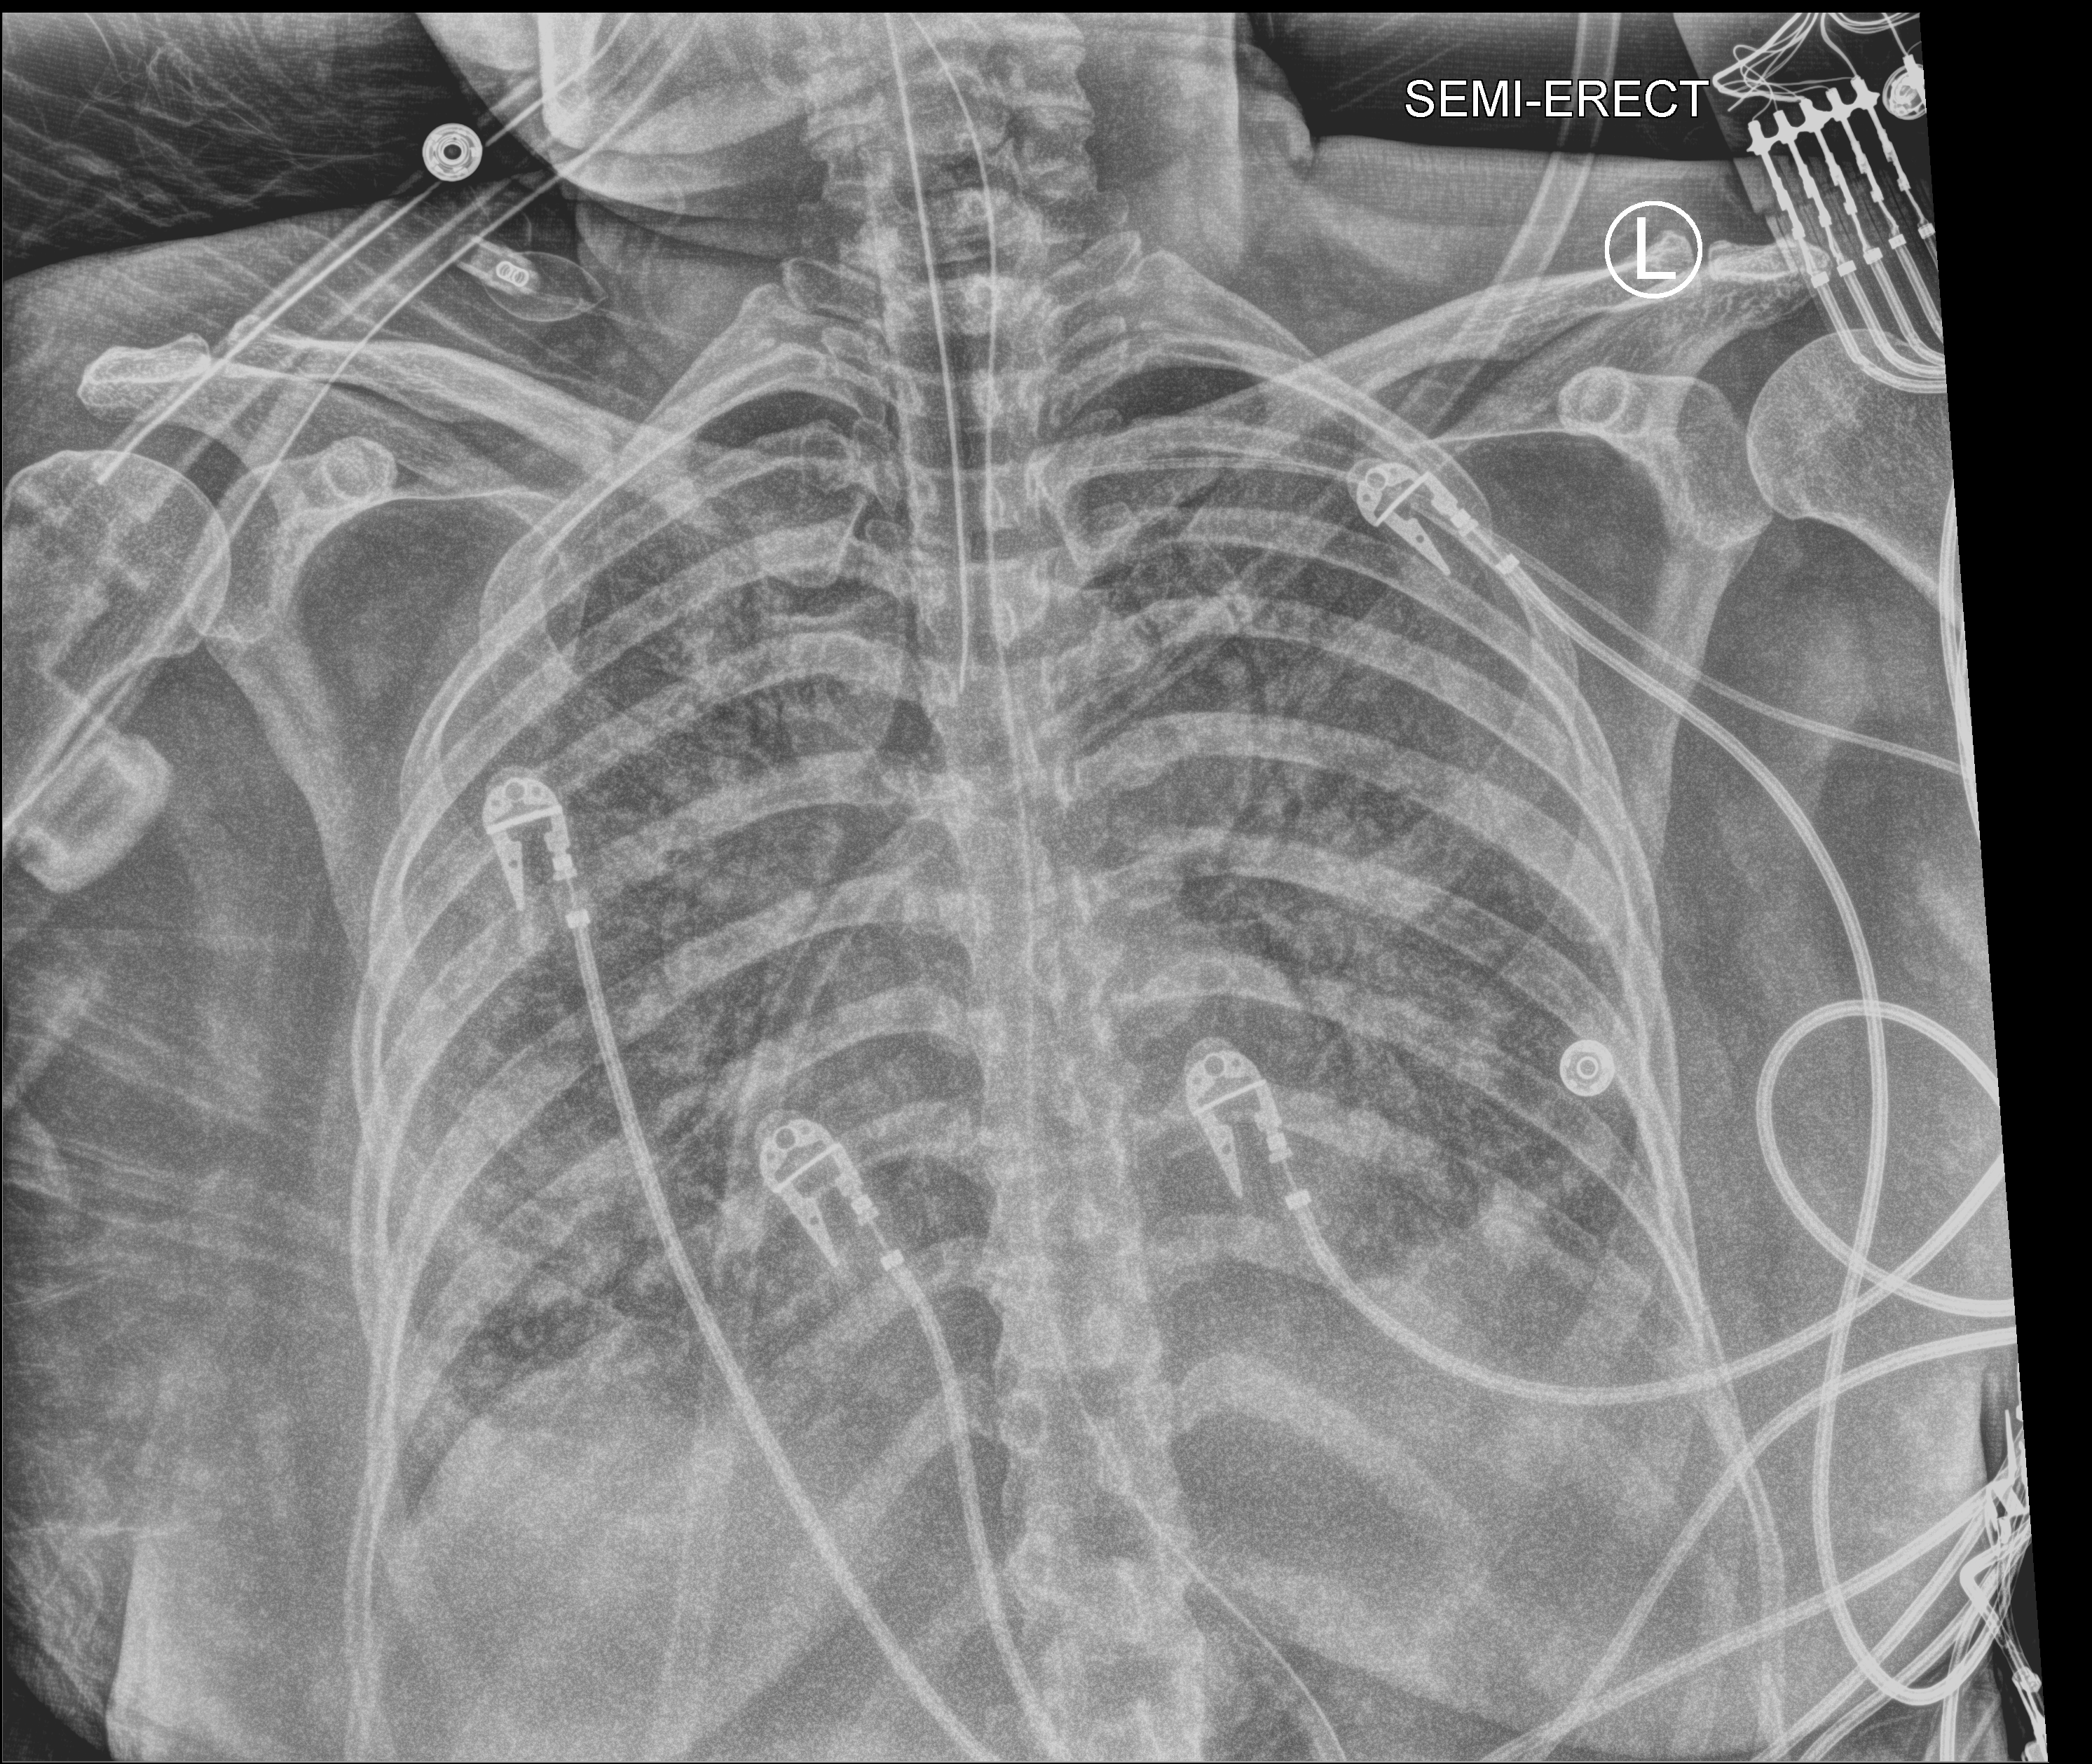
Portable chest radiograph, anteroposterior (AP) projection. Male patient hospitalised with COVID-19, age 18–59 years.
Admission-level facts for this patient (not findings on this image; timing relative to this image not recorded): admitted to intensive care during this hospital stay: yes; mechanically ventilated during this hospital stay: yes.